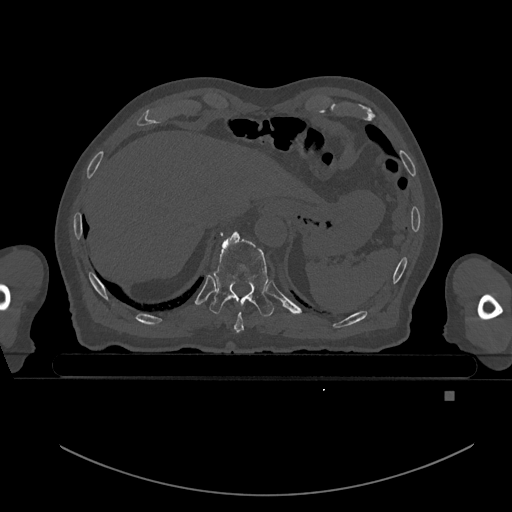
CT including the spine, one axial slice; bone window (W 1800 / L 400 HU); 0.5 mm slice thickness; 512 × 512 image matrix, field of view 456 × 456 mm. Patient: male, 82 years. Case-level facts recorded for this patient, not image findings: primary cancer: prostate; vertebrae with lytic lesions (as recorded): T11, T9, T8, T2.
Annotated regions visible in this slice (semi-automatic segmentation, software-assisted and operator-edited):
- T10 vertebra: bounding box (x1, y1, x2, y2) in pixels: (210, 231, 274, 317)
- T9 vertebra: (234, 312, 244, 333)